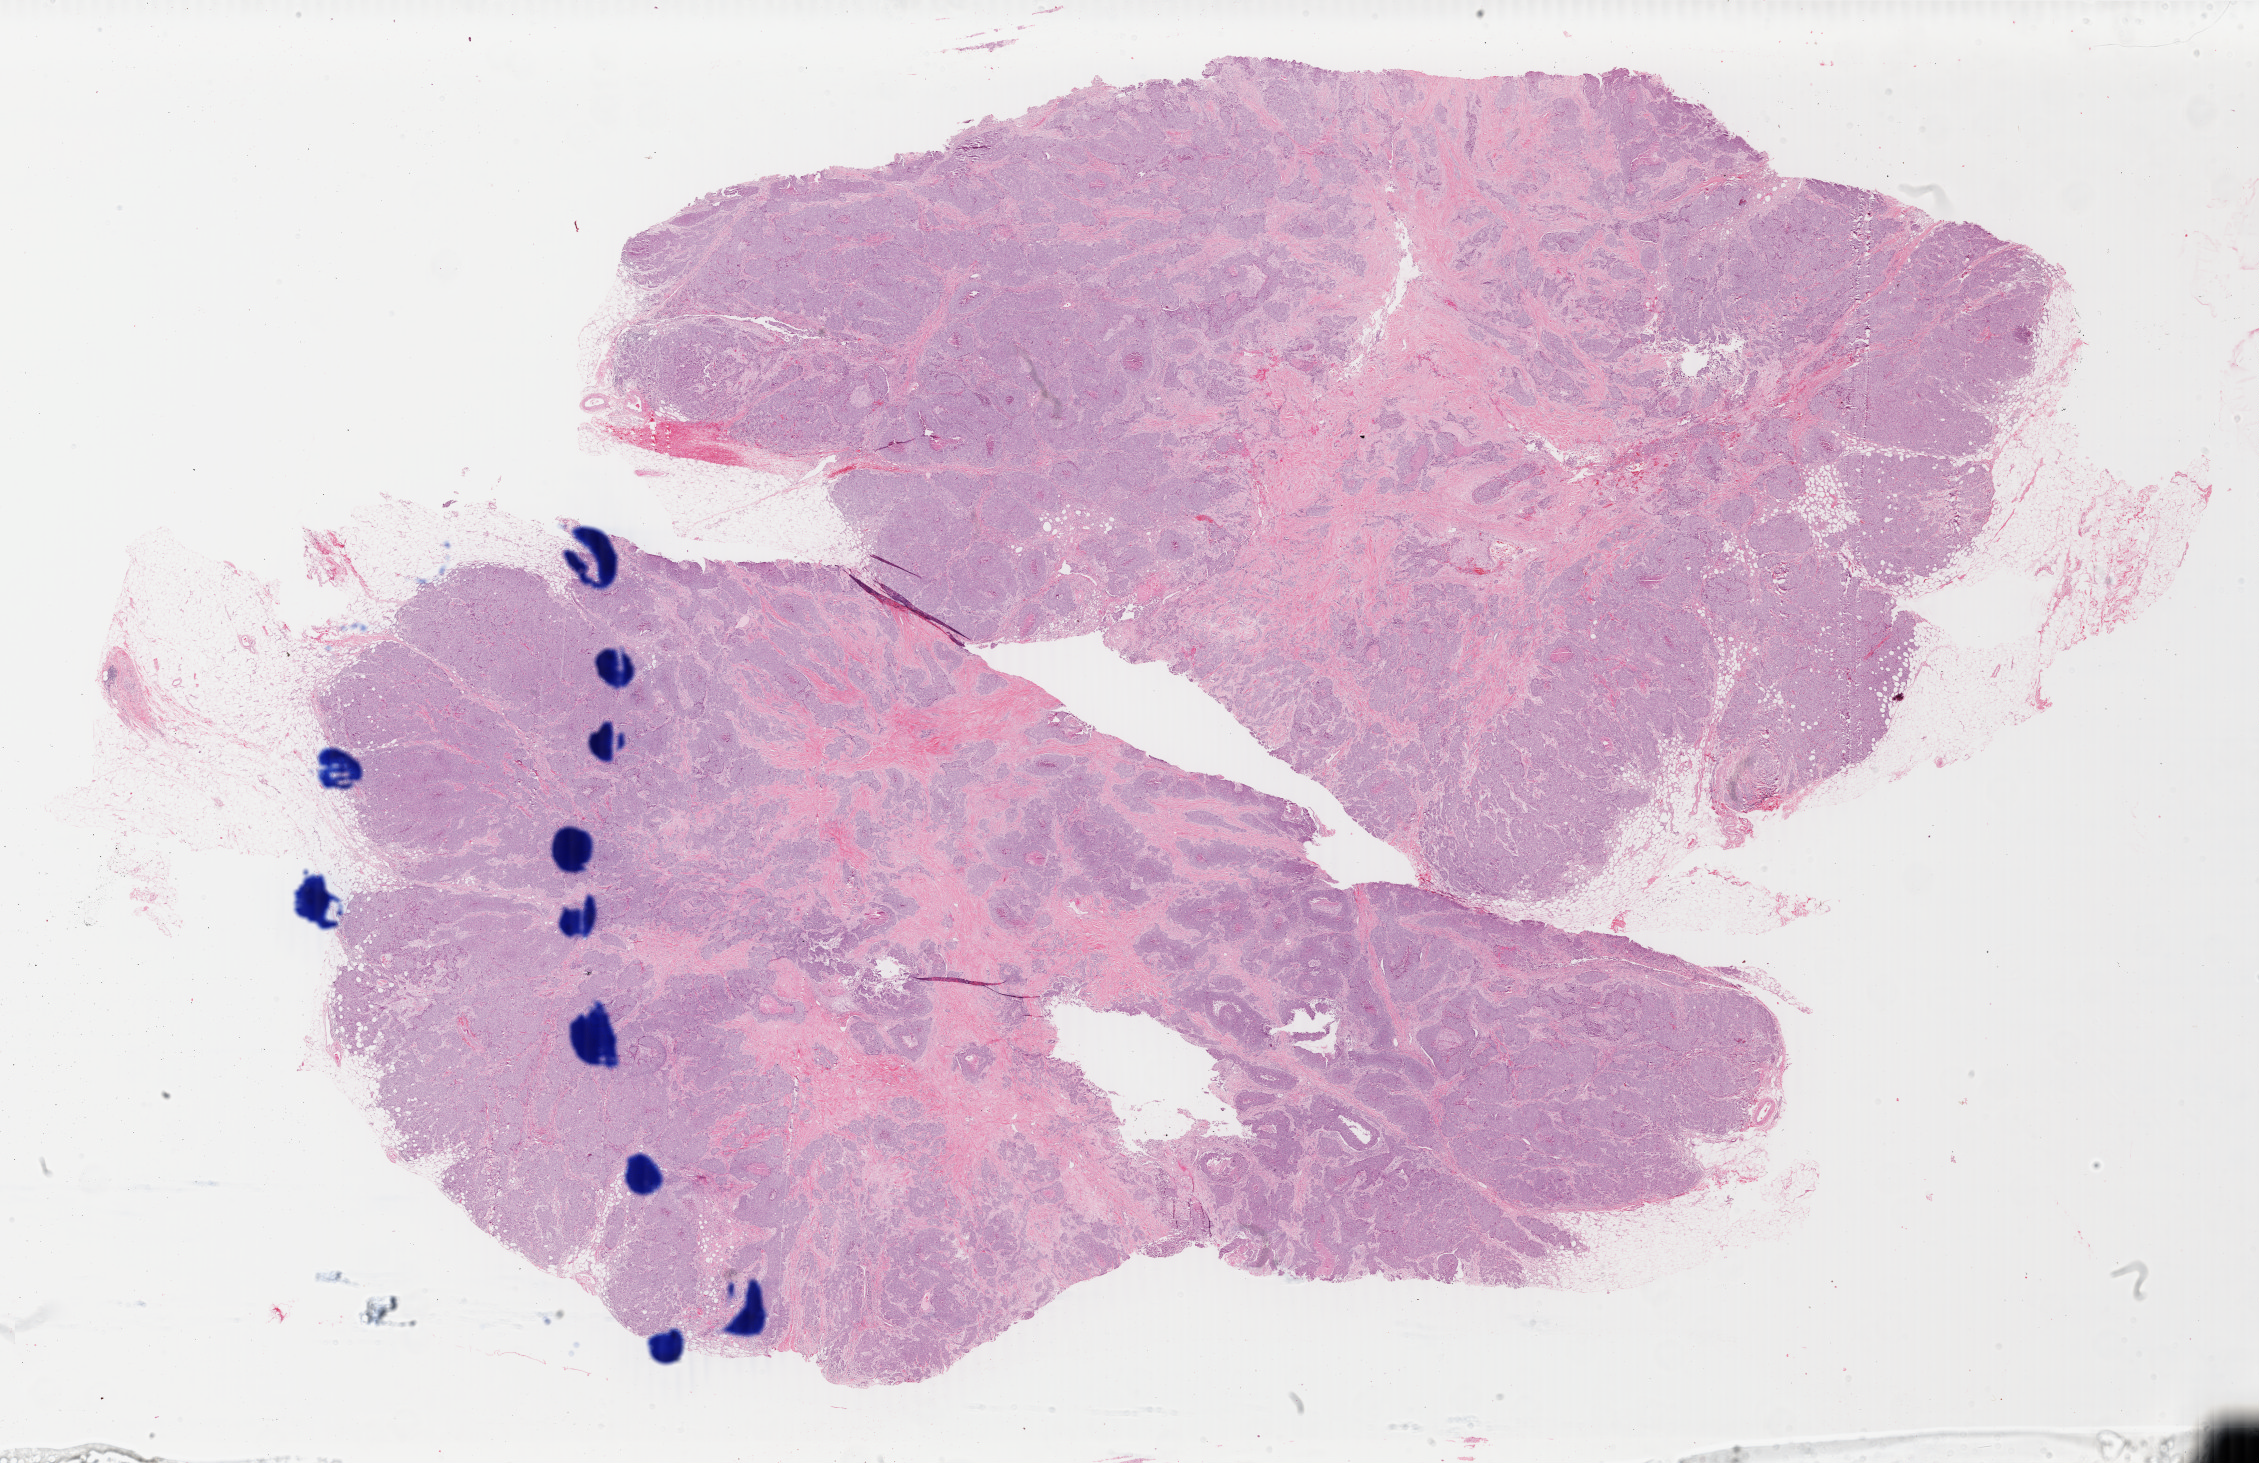
Whole-slide histology image, H&E, a low-resolution overview of the entire scanned area, about 35.9 x 23.3 mm; FFPE section; breast, primary tumour sample. Female, age 62 years at initial diagnosis.
Diagnosis: Infiltrating duct carcinoma, NOS. AJCC pathologic stage: IV (3rd edition).